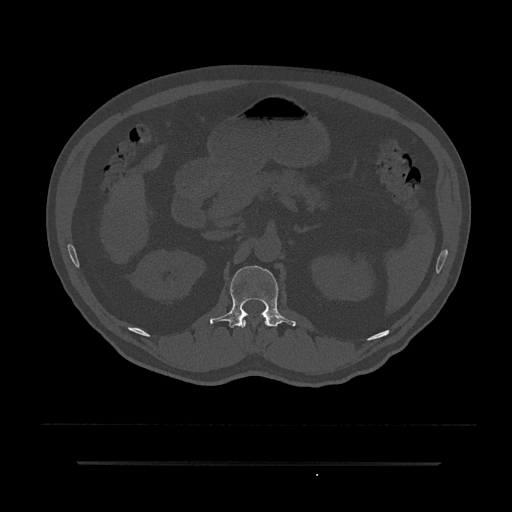
CT including the spine, one axial slice. Position 157 of 797 along the scan axis. Bone window (W 1800 / L 400 HU). 512 × 512 image matrix. Patient: male, 59 years. Case-level facts recorded for this patient, not image findings: primary cancer: bile ducts.
Structures marked on this image (semi-automatically segmented with operator editing):
- L1 vertebra: bounding box <210,265,296,328> (left, top, right, bottom; pixels)
- T12 vertebra: <241,320,268,328>